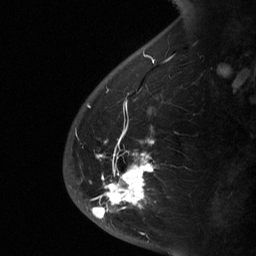
Breast MRI (dynamic contrast-enhanced), one sagittal slice; position 16 of 64 along the scan axis; dynamic contrast-enhanced study with each time point stored as its own series, time point 2 of 3 at this slice position (early post-contrast, ordered by acquisition time); 1.5 T; TE 4.8 ms, TR 27 ms; 2 mm slice thickness; 256 × 256 image matrix. Patient: female, 56 years. From the clinical record (not read from this slice): setting: breast cancer imaged before/during neoadjuvant chemotherapy; receptor status: HER2-positive.
Structures marked on this image (semi-automatic segmentation, software-assisted and operator-edited):
- analysis volume of interest (the breast-tissue region the enhancement analysis was run in; not a lesion): bounding box (x1, y1, x2, y2) in pixels: (63, 136, 181, 229)
- tumour enhancement mask (voxels above the 90 % enhancement threshold inside the analysis volume of interest): (92, 140, 155, 219)